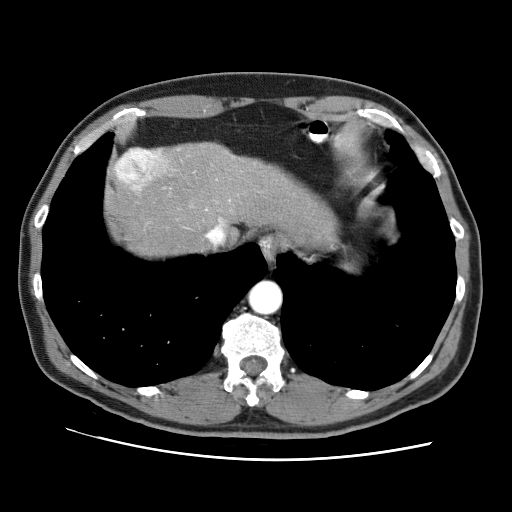
Contrast-enhanced abdominal CT (liver protocol), one axial slice. Position 61 of 71 along the scan axis. 120 kVp. Soft-tissue window (W 400 / L 40 HU). 2.5 mm slice thickness. 512 × 512 image matrix. From the clinical record (not read from this slice): diagnosis: hepatocellular carcinoma (patient treated with transarterial chemoembolisation; whether this scan precedes or follows treatment is not stated here); TNM stage (as recorded): Stage-II; Child-Pugh class: A; tumour size: 4.6 cm.
Annotated regions visible in this slice (semi-automatic segmentation, software-assisted and operator-edited):
- liver parenchyma outside the tumour (the mass and vessels are separate outlines, so this box may not span the whole liver): bounding box [x1, y1, x2, y2] px = [112, 142, 332, 256]
- mass: [115, 149, 167, 192]
- liver vessels: [219, 218, 223, 223]